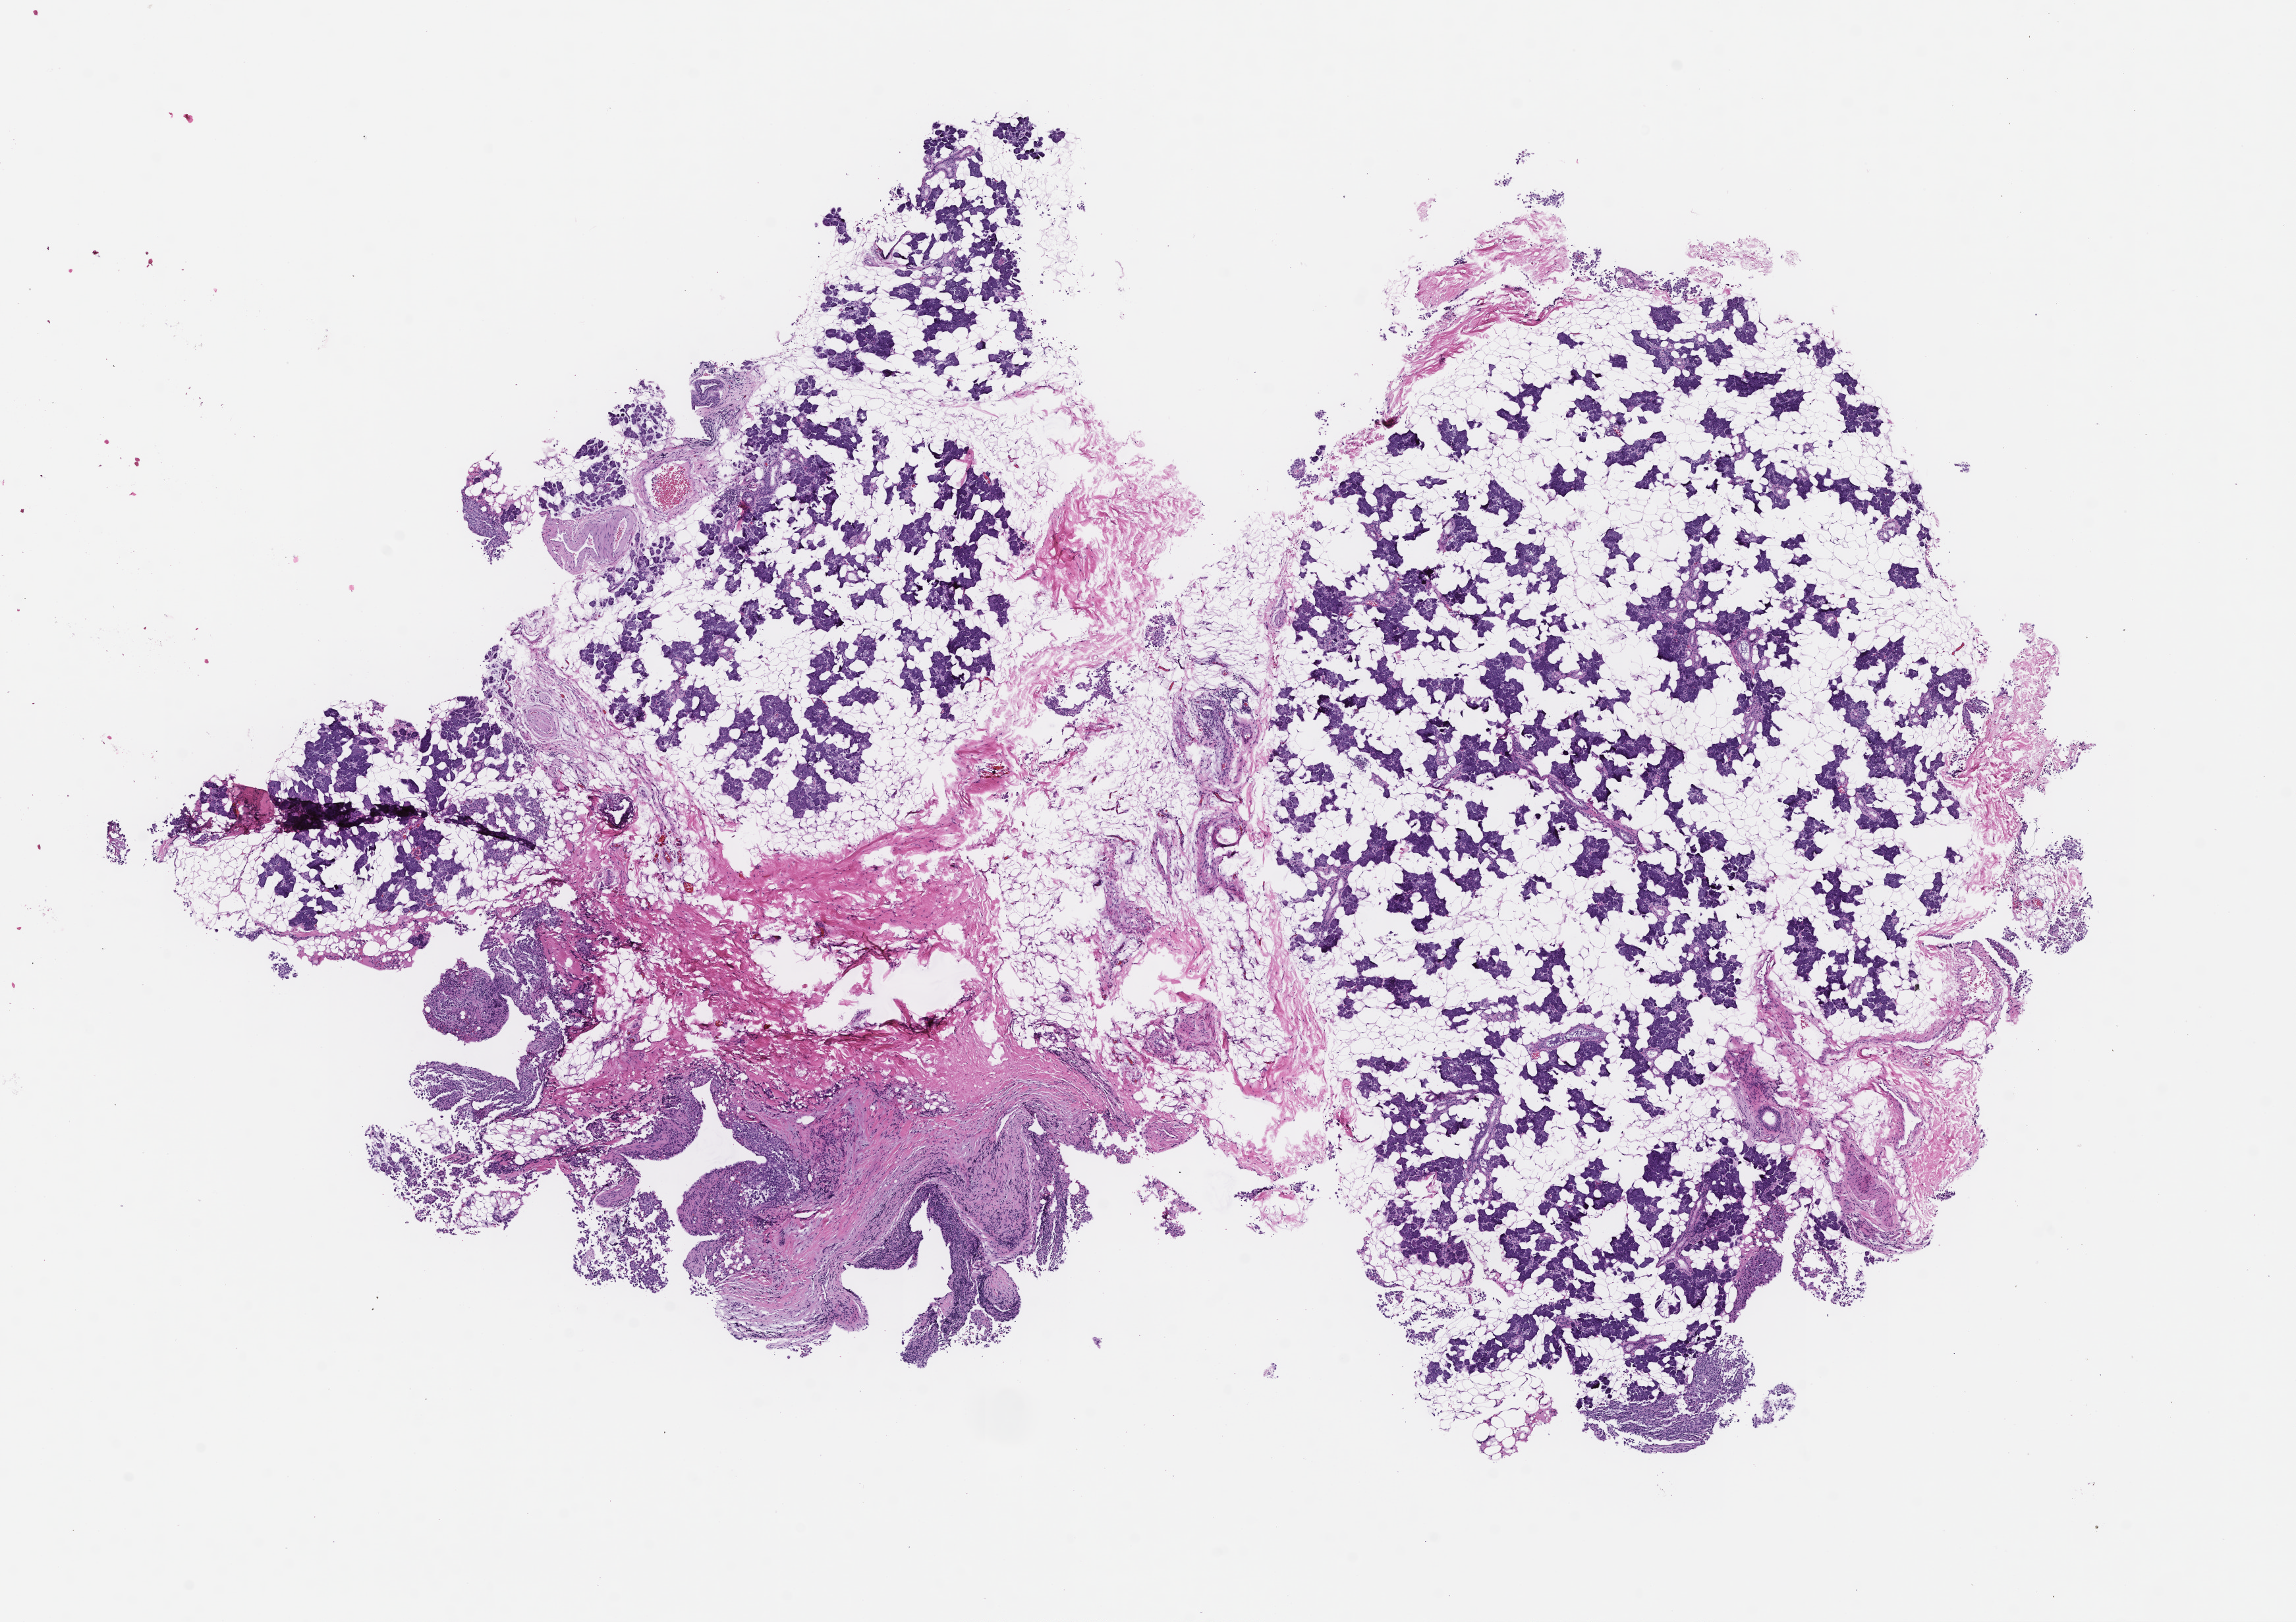
Whole-slide image, haematoxylin and eosin stain — a low-resolution overview of the entire scanned area, about 14.1 x 9.9 mm, formalin-fixed paraffin-embedded section. Male patient.
This section: metastasis (sampled organ not recorded). Patient diagnosis (primary): Melanoma.